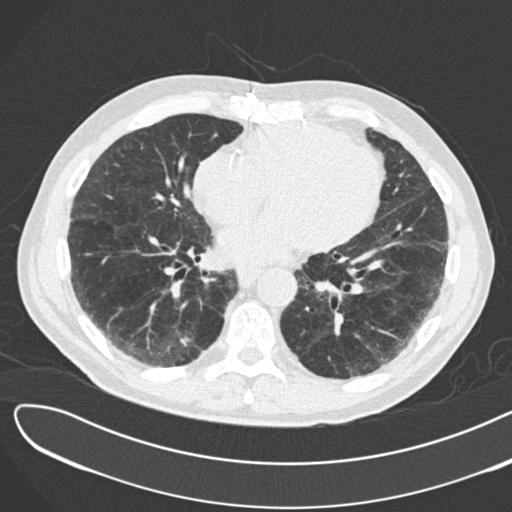
Low-dose screening chest CT, axial slice; second annual screen; lung window (W 1500 / L -600 HU); 2 mm slice thickness. Male participant, aged 72 years at enrolment. Former smoker at enrolment.
• Expert reader's lesion annotation, bounding box <165,325,205,361> (left, top, right, bottom; pixels).
• The screening reader recorded 2 non-calcified nodules or masses ≥4 mm on this exam; which of them this box marks is not recorded.
• Lung cancer was diagnosed 46 days after this screen: squamous cell carcinoma, NOS, right lower lobe, poorly differentiated (G3), stage IB (AJCC 6th edition), 42 mm at pathology.